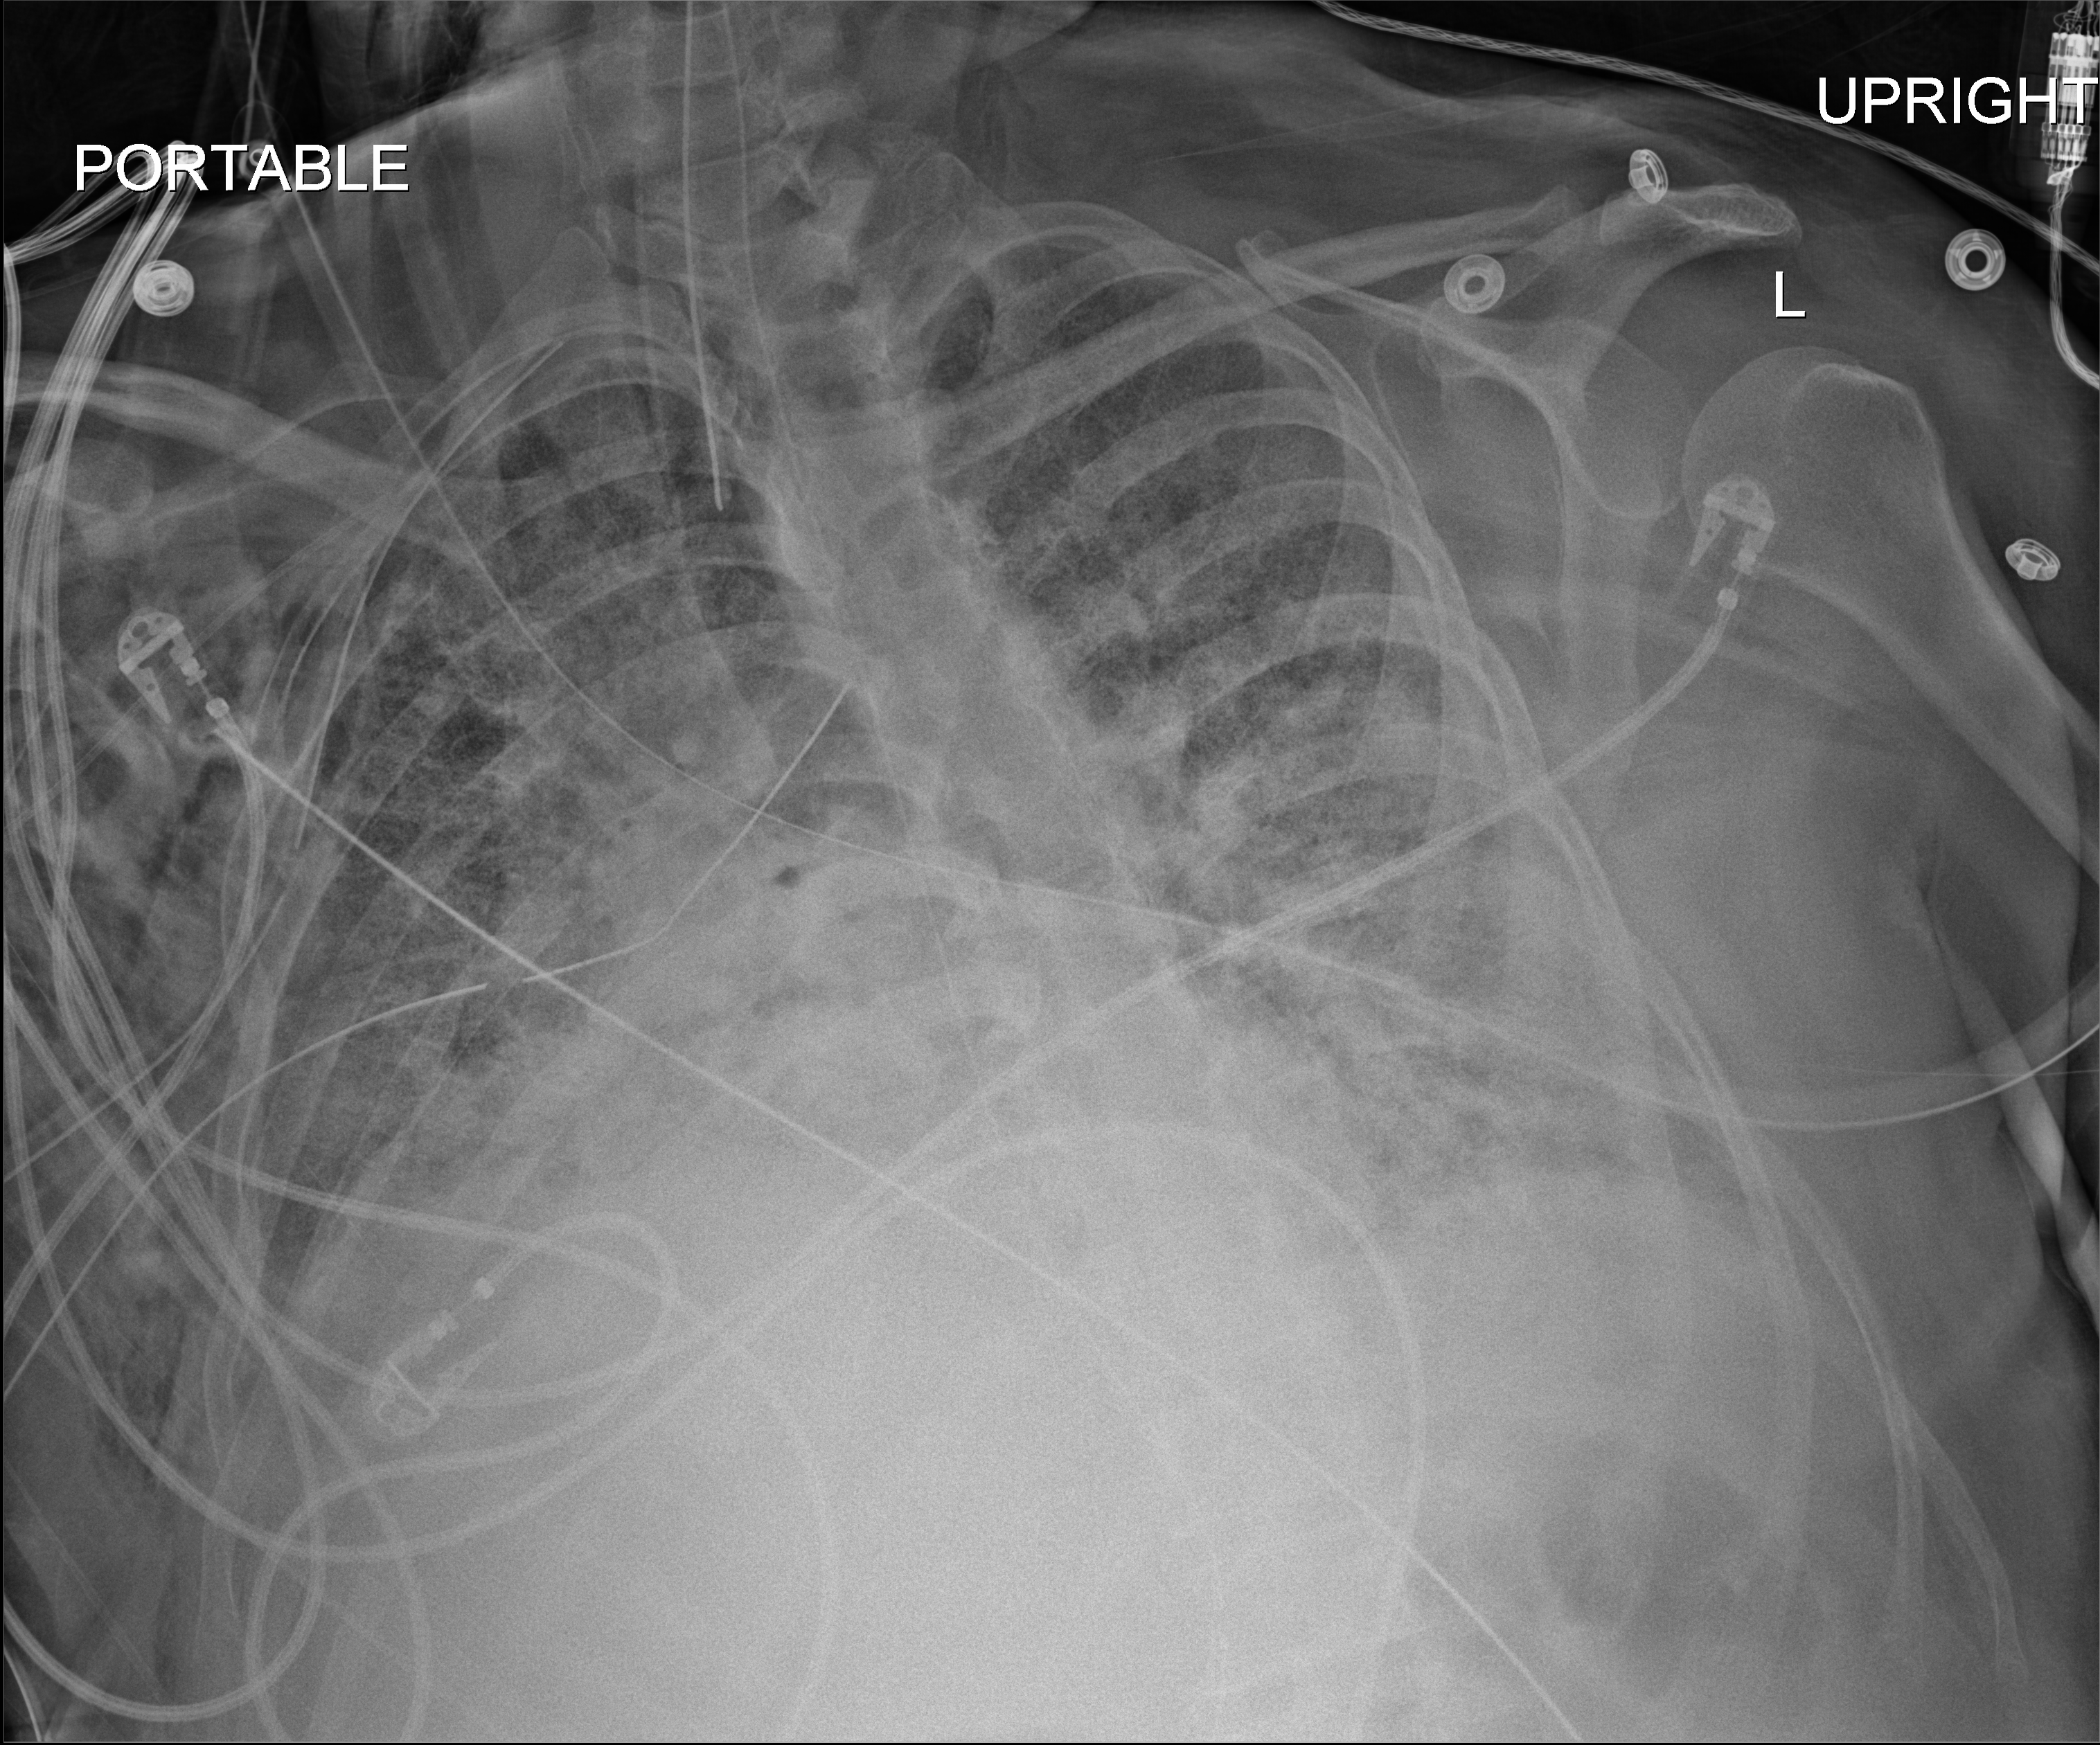
Portable chest radiograph; anteroposterior (AP) projection. Adult patient hospitalised with COVID-19, age 18–59 years.
Admission-level facts for this patient (not findings on this image; timing relative to this image not recorded):
- mechanically ventilated during this hospital stay: yes